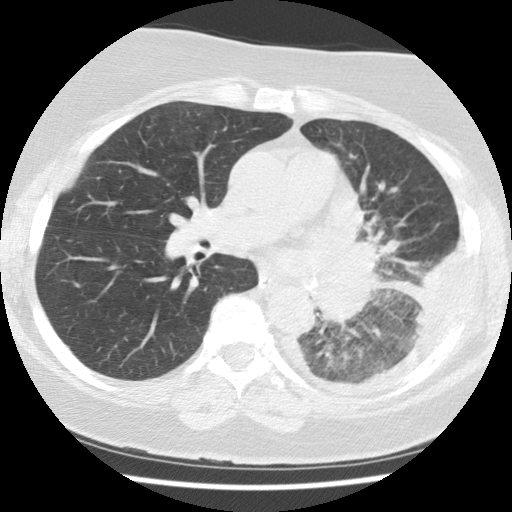
Low-dose screening chest CT, axial slice; first (baseline) screen; lung window (W 1500 / L -600 HU); 2.5 mm slice thickness; standard (soft-tissue) reconstruction kernel (STANDARD); slice 55 of 114 in the series. Female, age 65 years at enrolment. Current smoker at enrolment.
Expert-annotated lung lesion, bounding box (x1, y1, x2, y2) in pixels: (298, 283, 397, 360). Reader record for this screening exam (exam-level; its link to the box is not recorded): non-calcified nodule or mass ≥4 mm, left lower lobe, 74 × 48 mm, spiculated (stellate) margins, soft tissue attenuation. Official screen result: positive, change unspecified: nodule(s) >= 4 mm or enlarging nodule(s), mass(es), or other non-specific abnormalities suspicious for lung cancer. Later outcome: lung cancer diagnosed 13 days after this screen — adenocarcinoma, NOS, left lower lobe, stage IV (AJCC 6th edition), 74 mm at pathology.